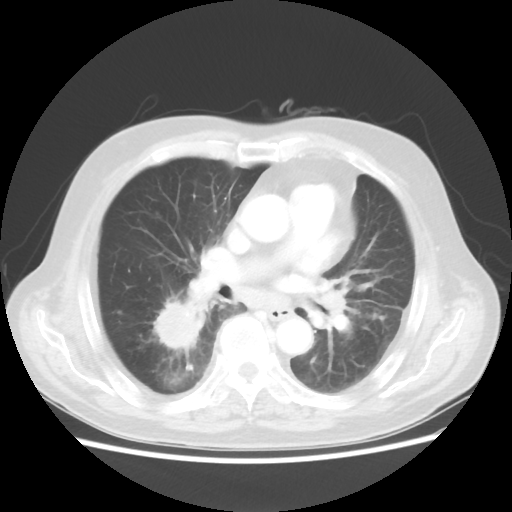
Chest CT, one axial slice. Position 21 of 44 along the scan axis. Reconstruction kernel STANDARD. 100 kVp. Lung window (W 1500 / L -600 HU). 5 mm slice thickness. 512 × 512 image matrix, field of view 359 × 359 mm. Male patient, age 83 years. Case-level facts recorded for this patient, not image findings: clinical TNM (as recorded): T2 N3 M0.
Structures marked on this image (rectangle marked by the reading radiologist):
- lung tumour (recorded histology: adenocarcinoma): box from (x=142, y=298) to (x=208, y=354) px